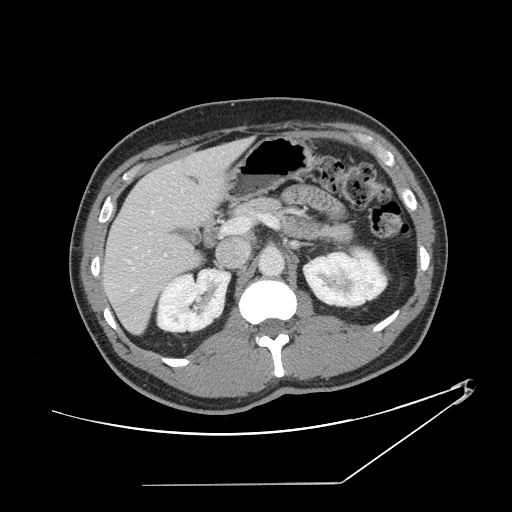
Contrast-enhanced abdominal CT, one axial slice. Slice 75 of 152 in the series (ordered by position). Intravenous contrast given. Soft-tissue window (W 400 / L 40 HU). 2.5 mm slice thickness. 512 × 512 image matrix. Male patient, age 45 years. Case-level facts recorded for this patient, not image findings: diagnosis: colorectal cancer liver metastases, imaged before liver resection; multiple liver metastases: no.
Outlined on this slice (manually delineated by an expert):
- hepatic veins: bounding box <131,160,201,292> (left, top, right, bottom; pixels)
- liver: <104,140,250,333>
- planned liver remnant (the part of the liver to remain after resection): <104,158,211,333>
- portal vein (with intrahepatic branches): <128,215,277,269>